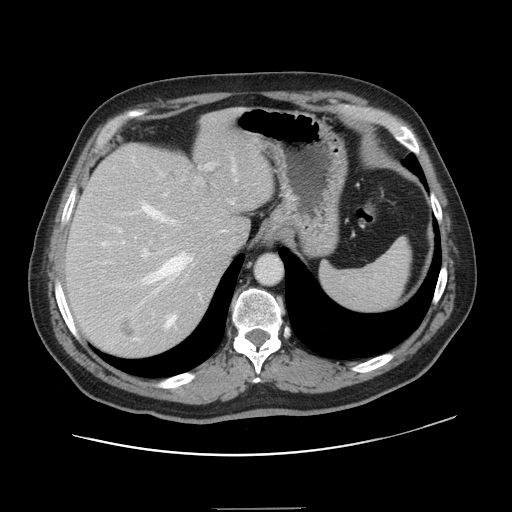
Contrast-enhanced abdominal CT, one axial slice. Slice 109 of 143 in the series (ordered by position). 120 kVp. Soft-tissue window (W 400 / L 40 HU). 2.5 mm slice thickness. 512 × 512 image matrix, field of view 402 × 402 mm. Male patient, age 62 years. Case-level facts recorded for this patient, not image findings: diagnosis: colorectal cancer liver metastases, imaged before liver resection; multiple liver metastases: yes; largest metastasis: 2.7 cm; chemotherapy before resection: yes.
Structures marked on this image (manually delineated by an expert):
- hepatic veins: bounding box (x1, y1, x2, y2) in pixels: (101, 168, 237, 327)
- liver: (67, 114, 273, 358)
- planned liver remnant (the part of the liver to remain after resection): (67, 113, 273, 275)
- portal vein (with intrahepatic branches): (118, 164, 212, 340)
- liver metastasis: (120, 322, 136, 337)
- liver metastasis: (169, 161, 179, 181)